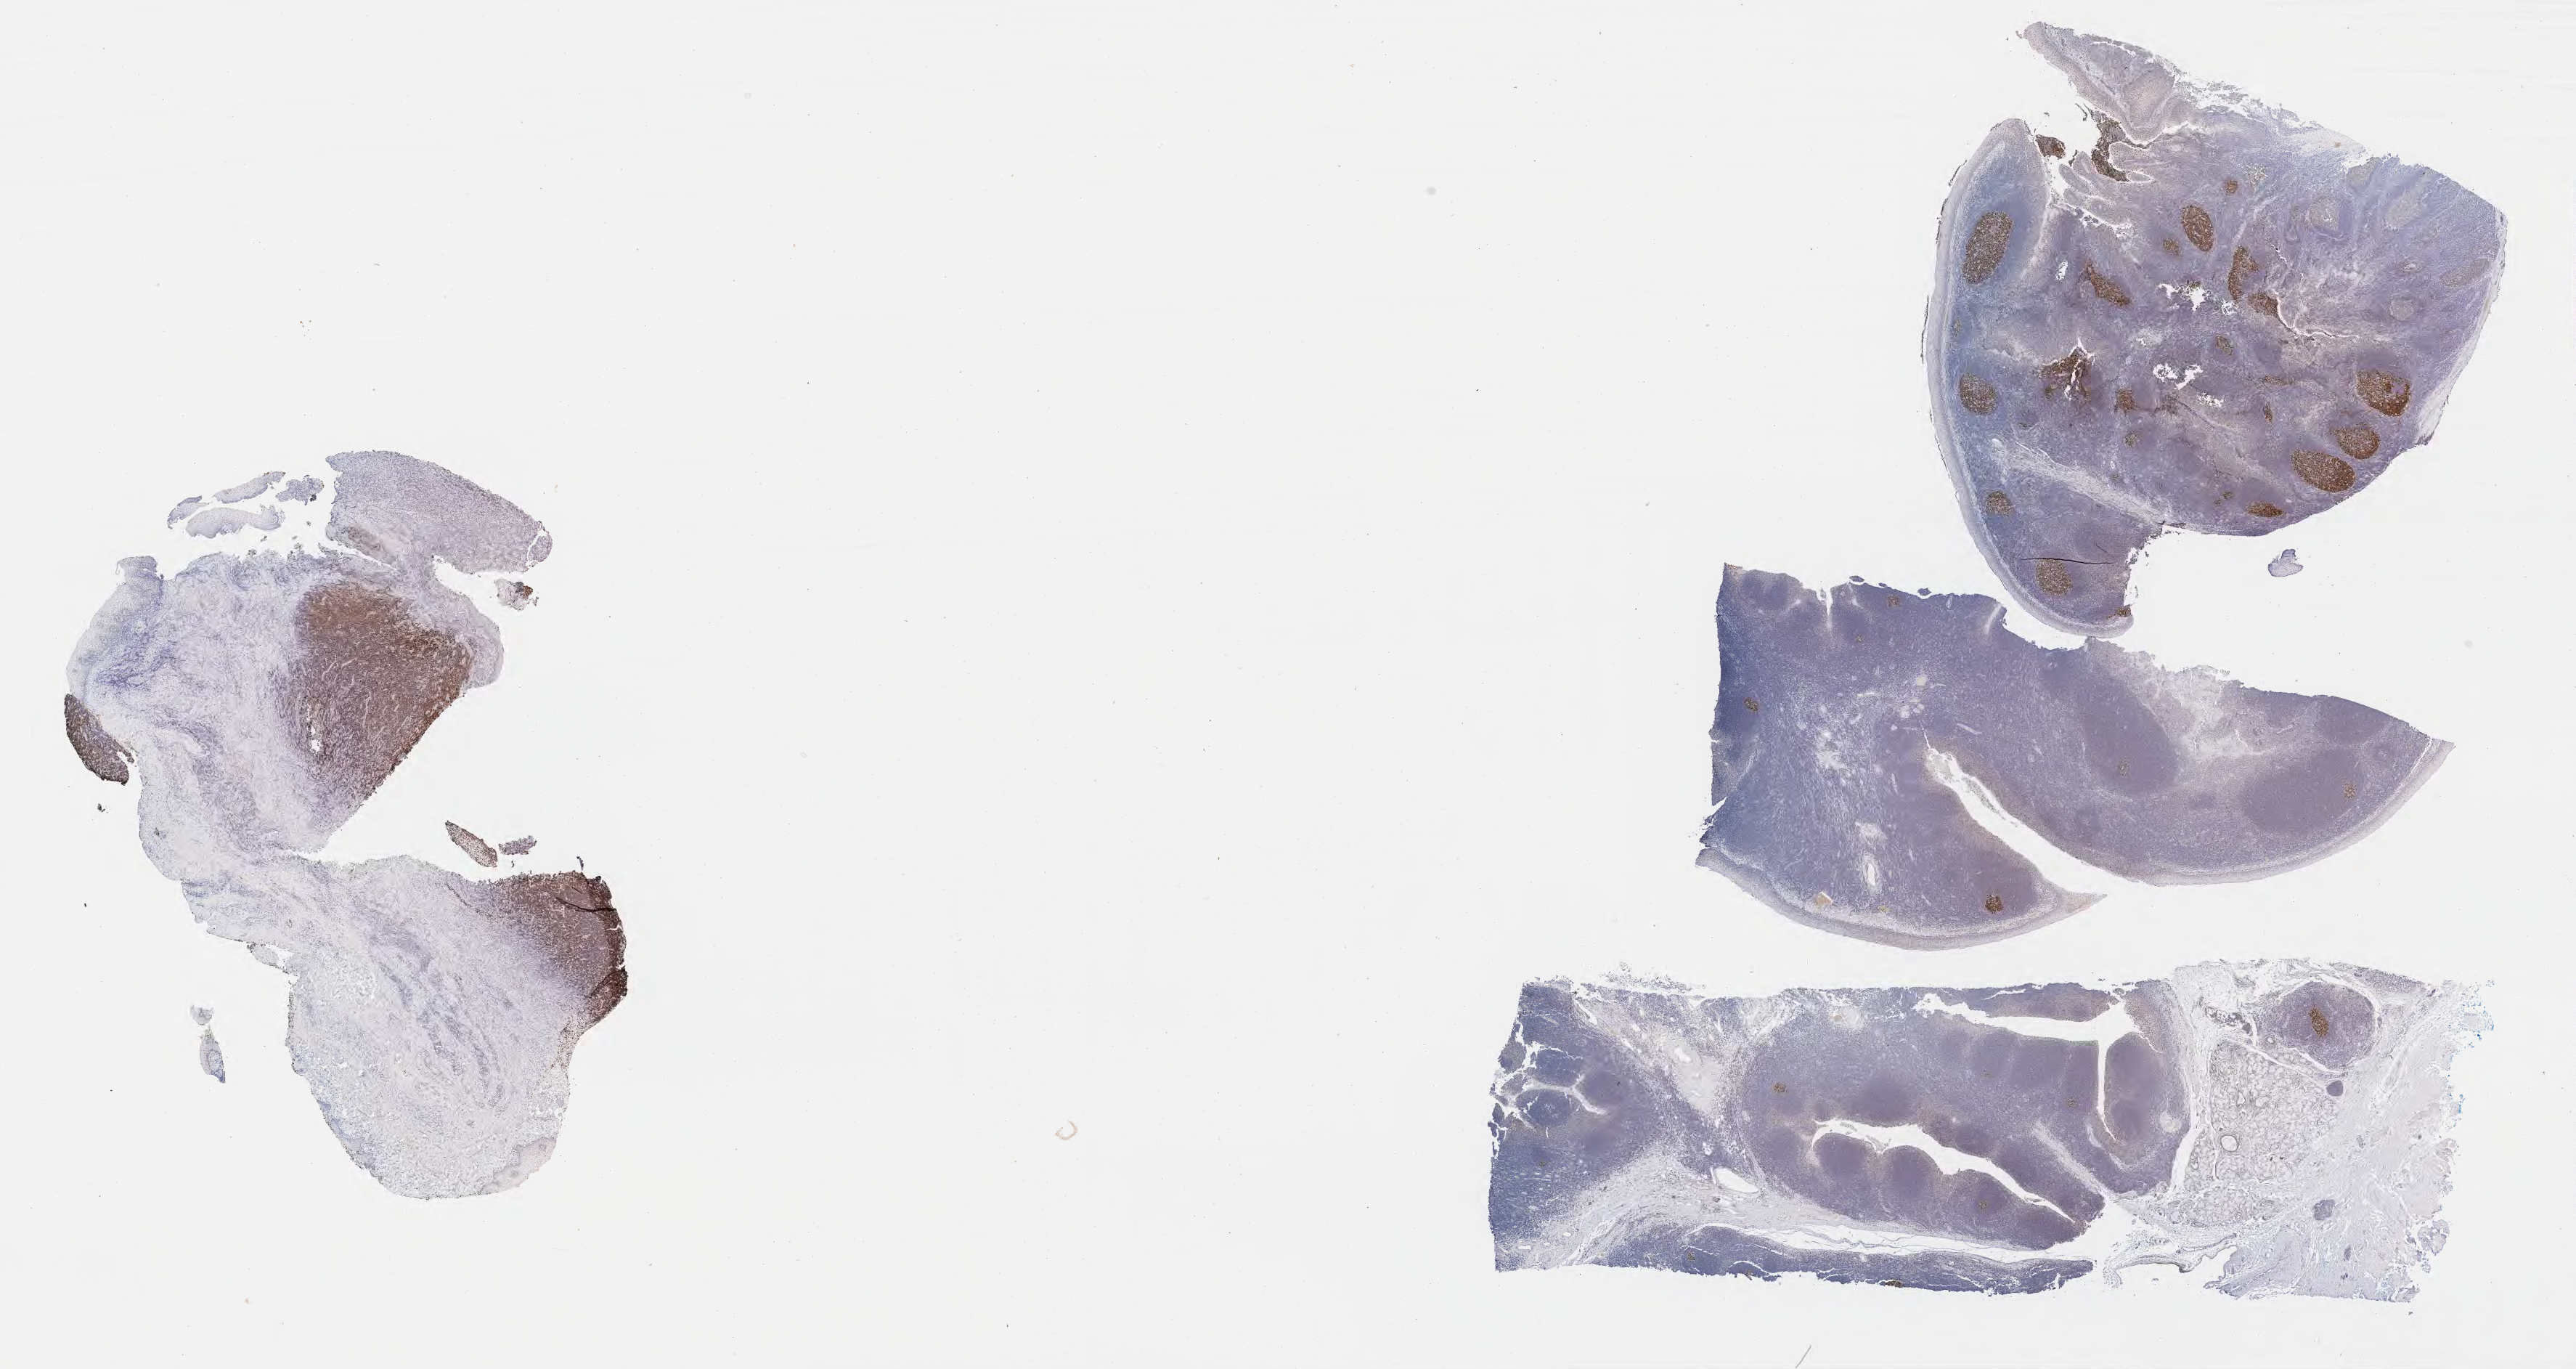
Immunohistochemistry (IHC) whole-slide image stained for BCL6 — shown as a low-resolution overview of the whole scanned area (about 28.7 x 15.2 mm); tumor tissue; anatomic site: cranium. Patient male; age 10 years.
- diagnosis: Burkitt lymphoma, NOS